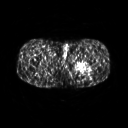
FDG PET of an extremity soft-tissue mass (from a PET/CT study), one axial slice; 3.27 mm slice thickness; 128 × 128 image matrix, field of view 500 × 500 mm. Patient: male, 27 years. From the clinical record (not read from this slice): histological type: extraskeletal osteosarcoma; grade: high; site of the primary tumour: left adductur.
Outlined on this slice (expert contour drawn on MRI and transferred to this co-registered scan by the dataset authors):
- gross tumour volume (mass): bounding box (x1, y1, x2, y2) in pixels: (72, 57, 95, 74)